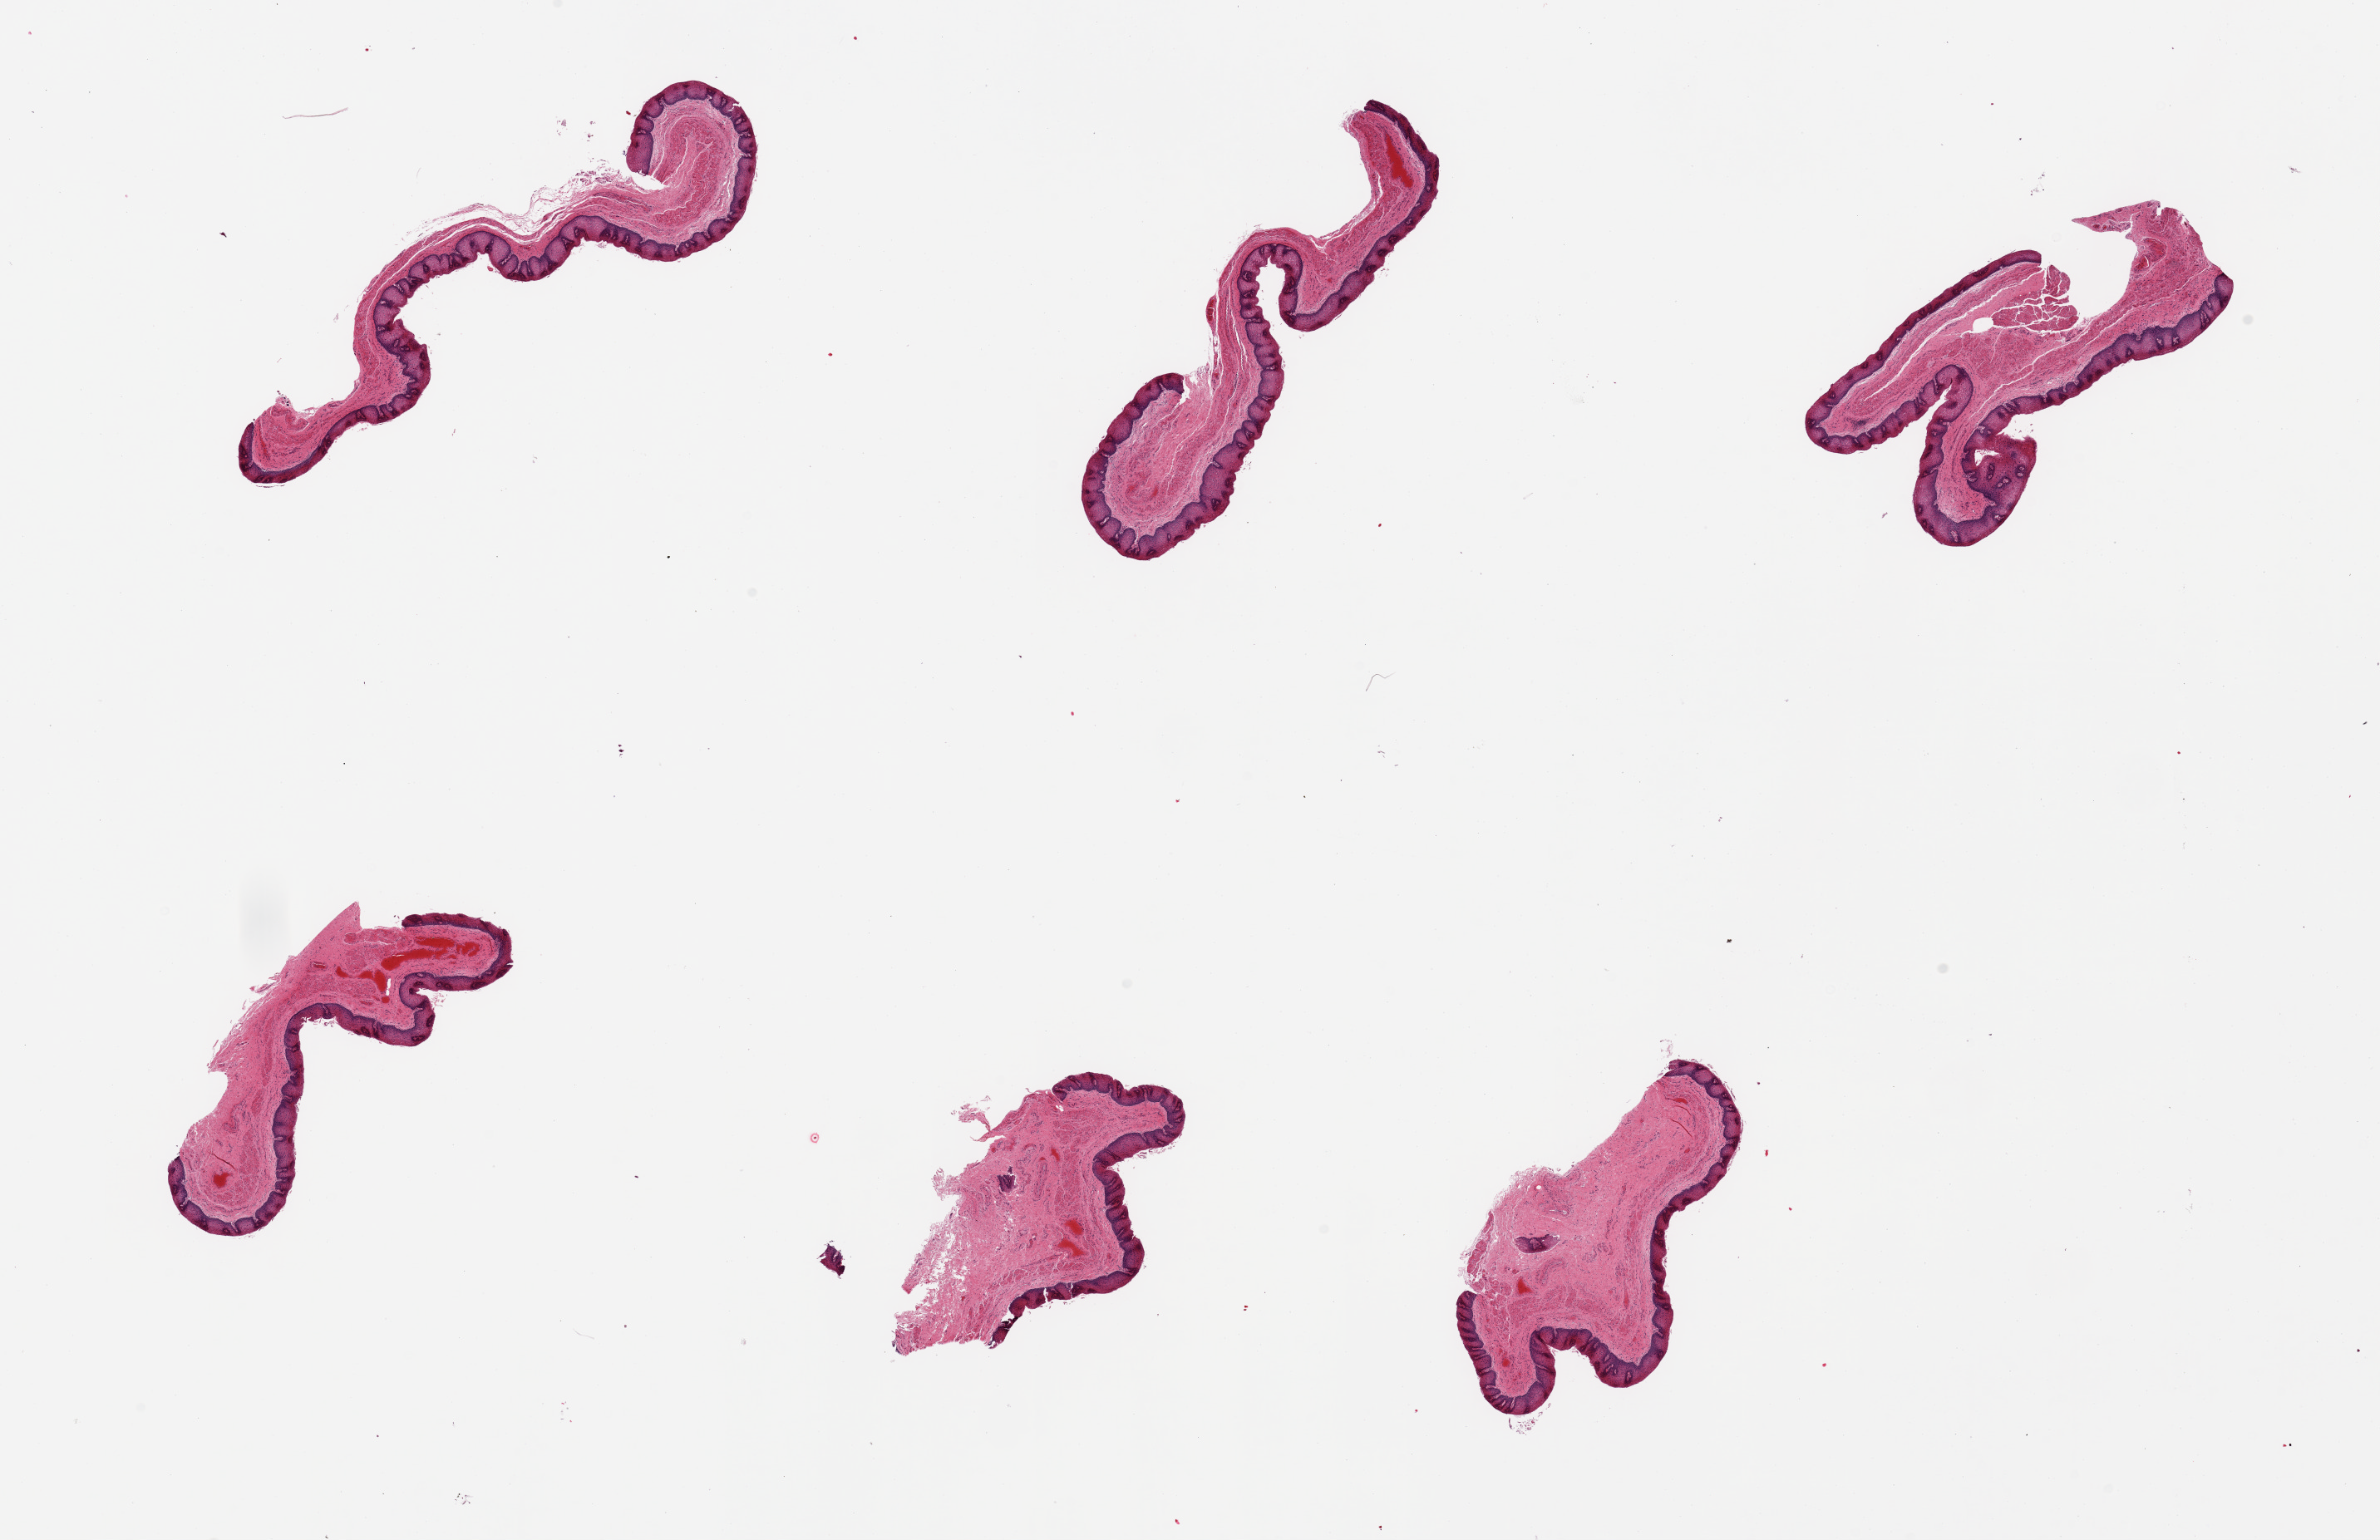
H&E whole-slide image, brightfield — shown as a low-resolution overview of the whole scanned area (about 22.6 x 14.7 mm); PAXgene-fixed, paraffin-embedded tissue; sampled site (target tissue): esophageal mucous membrane; tissue donor sample. Donor sex: male.
• review note (as recorded): 6 pieces, Squamous mucosa is ~0.2mm, ~20-25% thickness